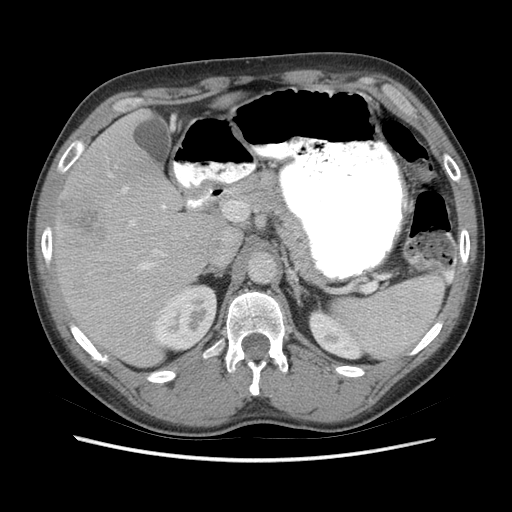
Contrast-enhanced abdominal CT (liver protocol), one axial slice; reconstruction kernel STANDARD; 140 kVp; soft-tissue window (W 400 / L 40 HU); 2.5 mm slice thickness; 512 × 512 image matrix. From the clinical record (not read from this slice): diagnosis: hepatocellular carcinoma (patient treated with transarterial chemoembolisation; whether this scan precedes or follows treatment is not stated here); TNM stage (as recorded): Stage-IIIA; Child-Pugh class: A; tumour size: 6.6 cm.
Structures marked on this image (semi-automatic segmentation, software-assisted and operator-edited):
- liver parenchyma outside the tumour (the mass and vessels are separate outlines, so this box may not span the whole liver): bounding box [x1, y1, x2, y2] px = [52, 96, 242, 366]
- mass: [58, 196, 108, 255]
- liver vessels: [109, 175, 224, 270]